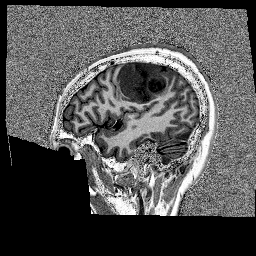
Brain MRI from a brain-tumour surgery series, one sagittal slice; slice 44 of 176 in the series (ordered by position); 256 × 256 image matrix, field of view 256 × 256 mm. Case-level facts recorded for this patient, not image findings: histopathology: Glioblastoma; WHO grade: 4; IDH mutation: no.
Outlined on this slice (expert manual segmentation):
- tumour: bounding box <118,61,175,103> (left, top, right, bottom; pixels)